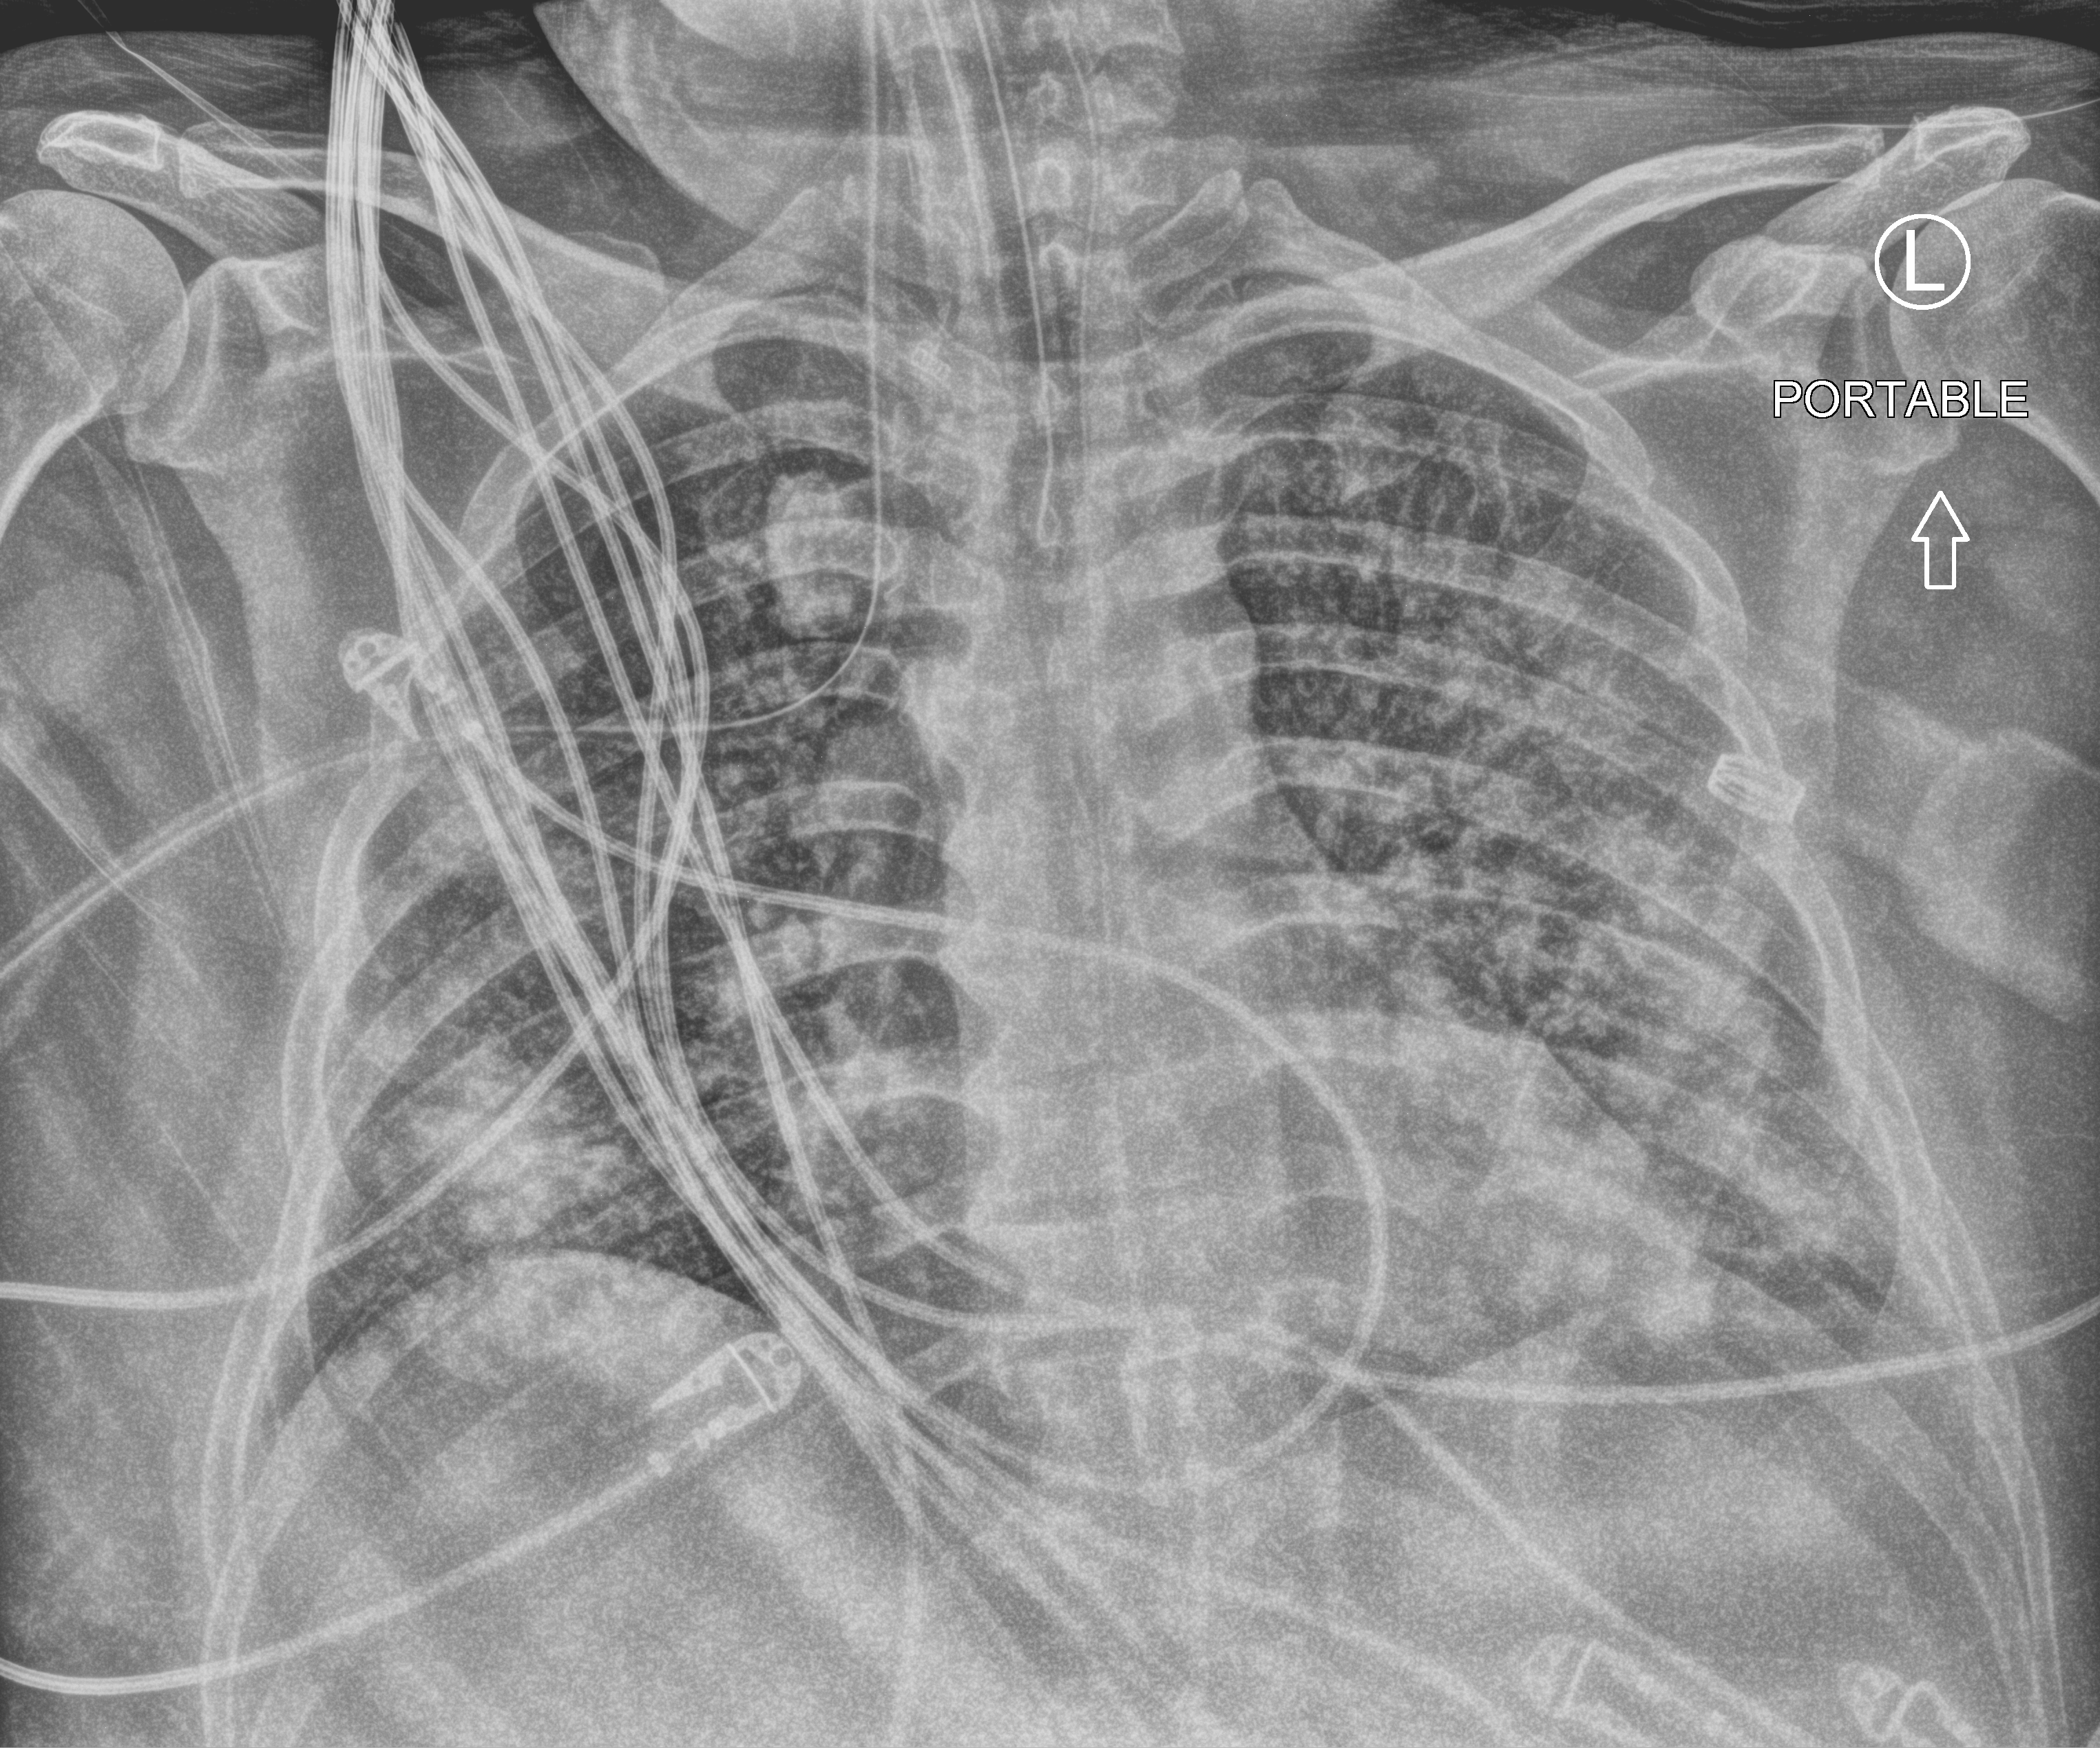
Portable chest radiograph, anteroposterior (AP) projection. Male patient hospitalised with COVID-19, age 18–59 years.
Admission-level facts for this patient (not findings on this image; timing relative to this image not recorded): admitted to intensive care during this hospital stay: yes; chronic kidney disease (admission record): no.